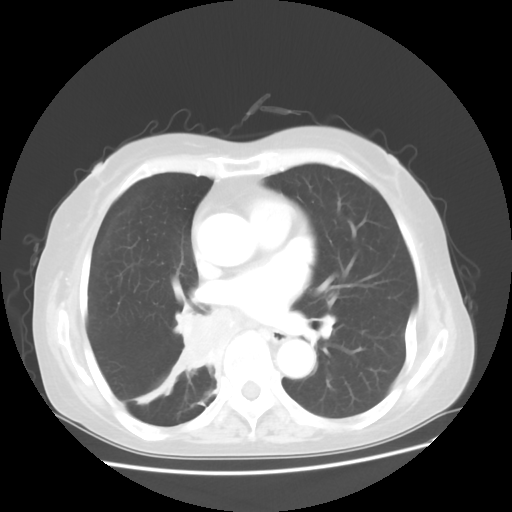
Chest CT, one axial slice. Slice 23 of 48 in the series (ordered by position). Reconstruction kernel STANDARD. 120 kVp. Lung window (W 1500 / L -600 HU). 5 mm slice thickness. 512 × 512 image matrix, field of view 360 × 360 mm. Female patient, age 63 years. Case-level facts recorded for this patient, not image findings: clinical TNM (as recorded): T2 N3 M1b; histopathological grade: G3.
Outlined on this slice (bounding box drawn by a radiologist):
- lung tumour (recorded histology: small cell carcinoma): box from (x=174, y=300) to (x=224, y=375) px